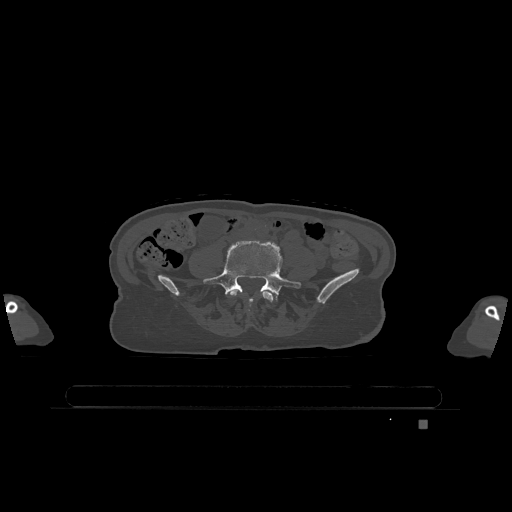
CT including the spine, one axial slice; position 255 of 1317 along the scan axis; bone window (W 1800 / L 400 HU); 0.5 mm slice thickness; 512 × 512 image matrix, field of view 500 × 500 mm. Female patient, age 74 years. From the clinical record (not read from this slice): primary cancer: lung; vertebrae with lytic lesions (as recorded): T1, T4, T5, T6, L4, L5.
Structures marked on this image (semi-automatically segmented with operator editing):
- L4 vertebra: bounding box <230,290,274,312> (left, top, right, bottom; pixels)
- L5 vertebra: <204,241,301,302>